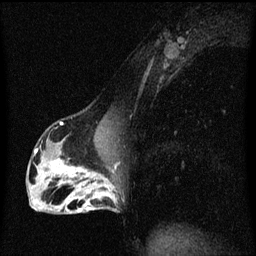
Breast MRI (dynamic contrast-enhanced), one sagittal slice; slice 30 of 60 in the series (ordered by position); dynamic contrast-enhanced series, image 2 of 3 at this slice position (ordered by acquisition); 1.5 T; TE 4.2 ms, TR 8.4 ms; 2 mm slice thickness; 256 × 256 image matrix. Patient: female, 40 years.
Annotated regions visible in this slice (semi-automatic segmentation, software-assisted and operator-edited):
- analysis volume of interest (the breast-tissue region the enhancement analysis was run in; not a lesion): bounding box (x1, y1, x2, y2) in pixels: (76, 172, 117, 213)
- tumour enhancement mask (voxels above the 70 % enhancement threshold inside the analysis volume of interest): (76, 172, 116, 213)